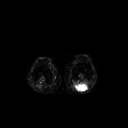
FDG PET of an extremity soft-tissue mass (from a PET/CT study), one axial slice. Position 177 of 267 along the scan axis. 128 × 128 image matrix. Patient: male, 54 years. From the clinical record (not read from this slice): histological type: synovial sarcoma; site of the primary tumour: left poplietal fossa.
Annotated regions visible in this slice (expert contour drawn on MRI and transferred to this co-registered scan by the dataset authors):
- gross tumour volume (mass): bounding box (x1, y1, x2, y2) in pixels: (77, 83, 89, 91)